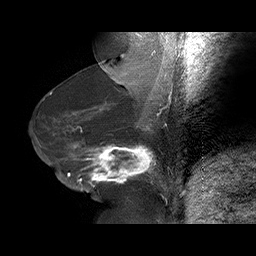
Breast MRI (dynamic contrast-enhanced), one sagittal slice; slice 33 of 75 in the series (ordered by position); dynamic contrast-enhanced series, time point 2 of 6 at this slice position (early post-contrast); 1.5 T; TE 4.5 ms, TR 32.4 ms; 3 mm slice thickness; 256 × 256 image matrix, field of view 180 × 180 mm. Female patient. Case-level facts recorded for this patient, not image findings: setting: breast cancer imaged before/during neoadjuvant chemotherapy; receptor status: HR-positive, HER2-negative.
Annotated regions visible in this slice (semi-automatic segmentation, software-assisted and operator-edited):
- analysis volume of interest (the breast-tissue region the enhancement analysis was run in; not a lesion): bounding box <58,134,166,191> (left, top, right, bottom; pixels)
- tumour enhancement mask (voxels above the 100 % enhancement threshold inside the analysis volume of interest): <67,143,157,186>